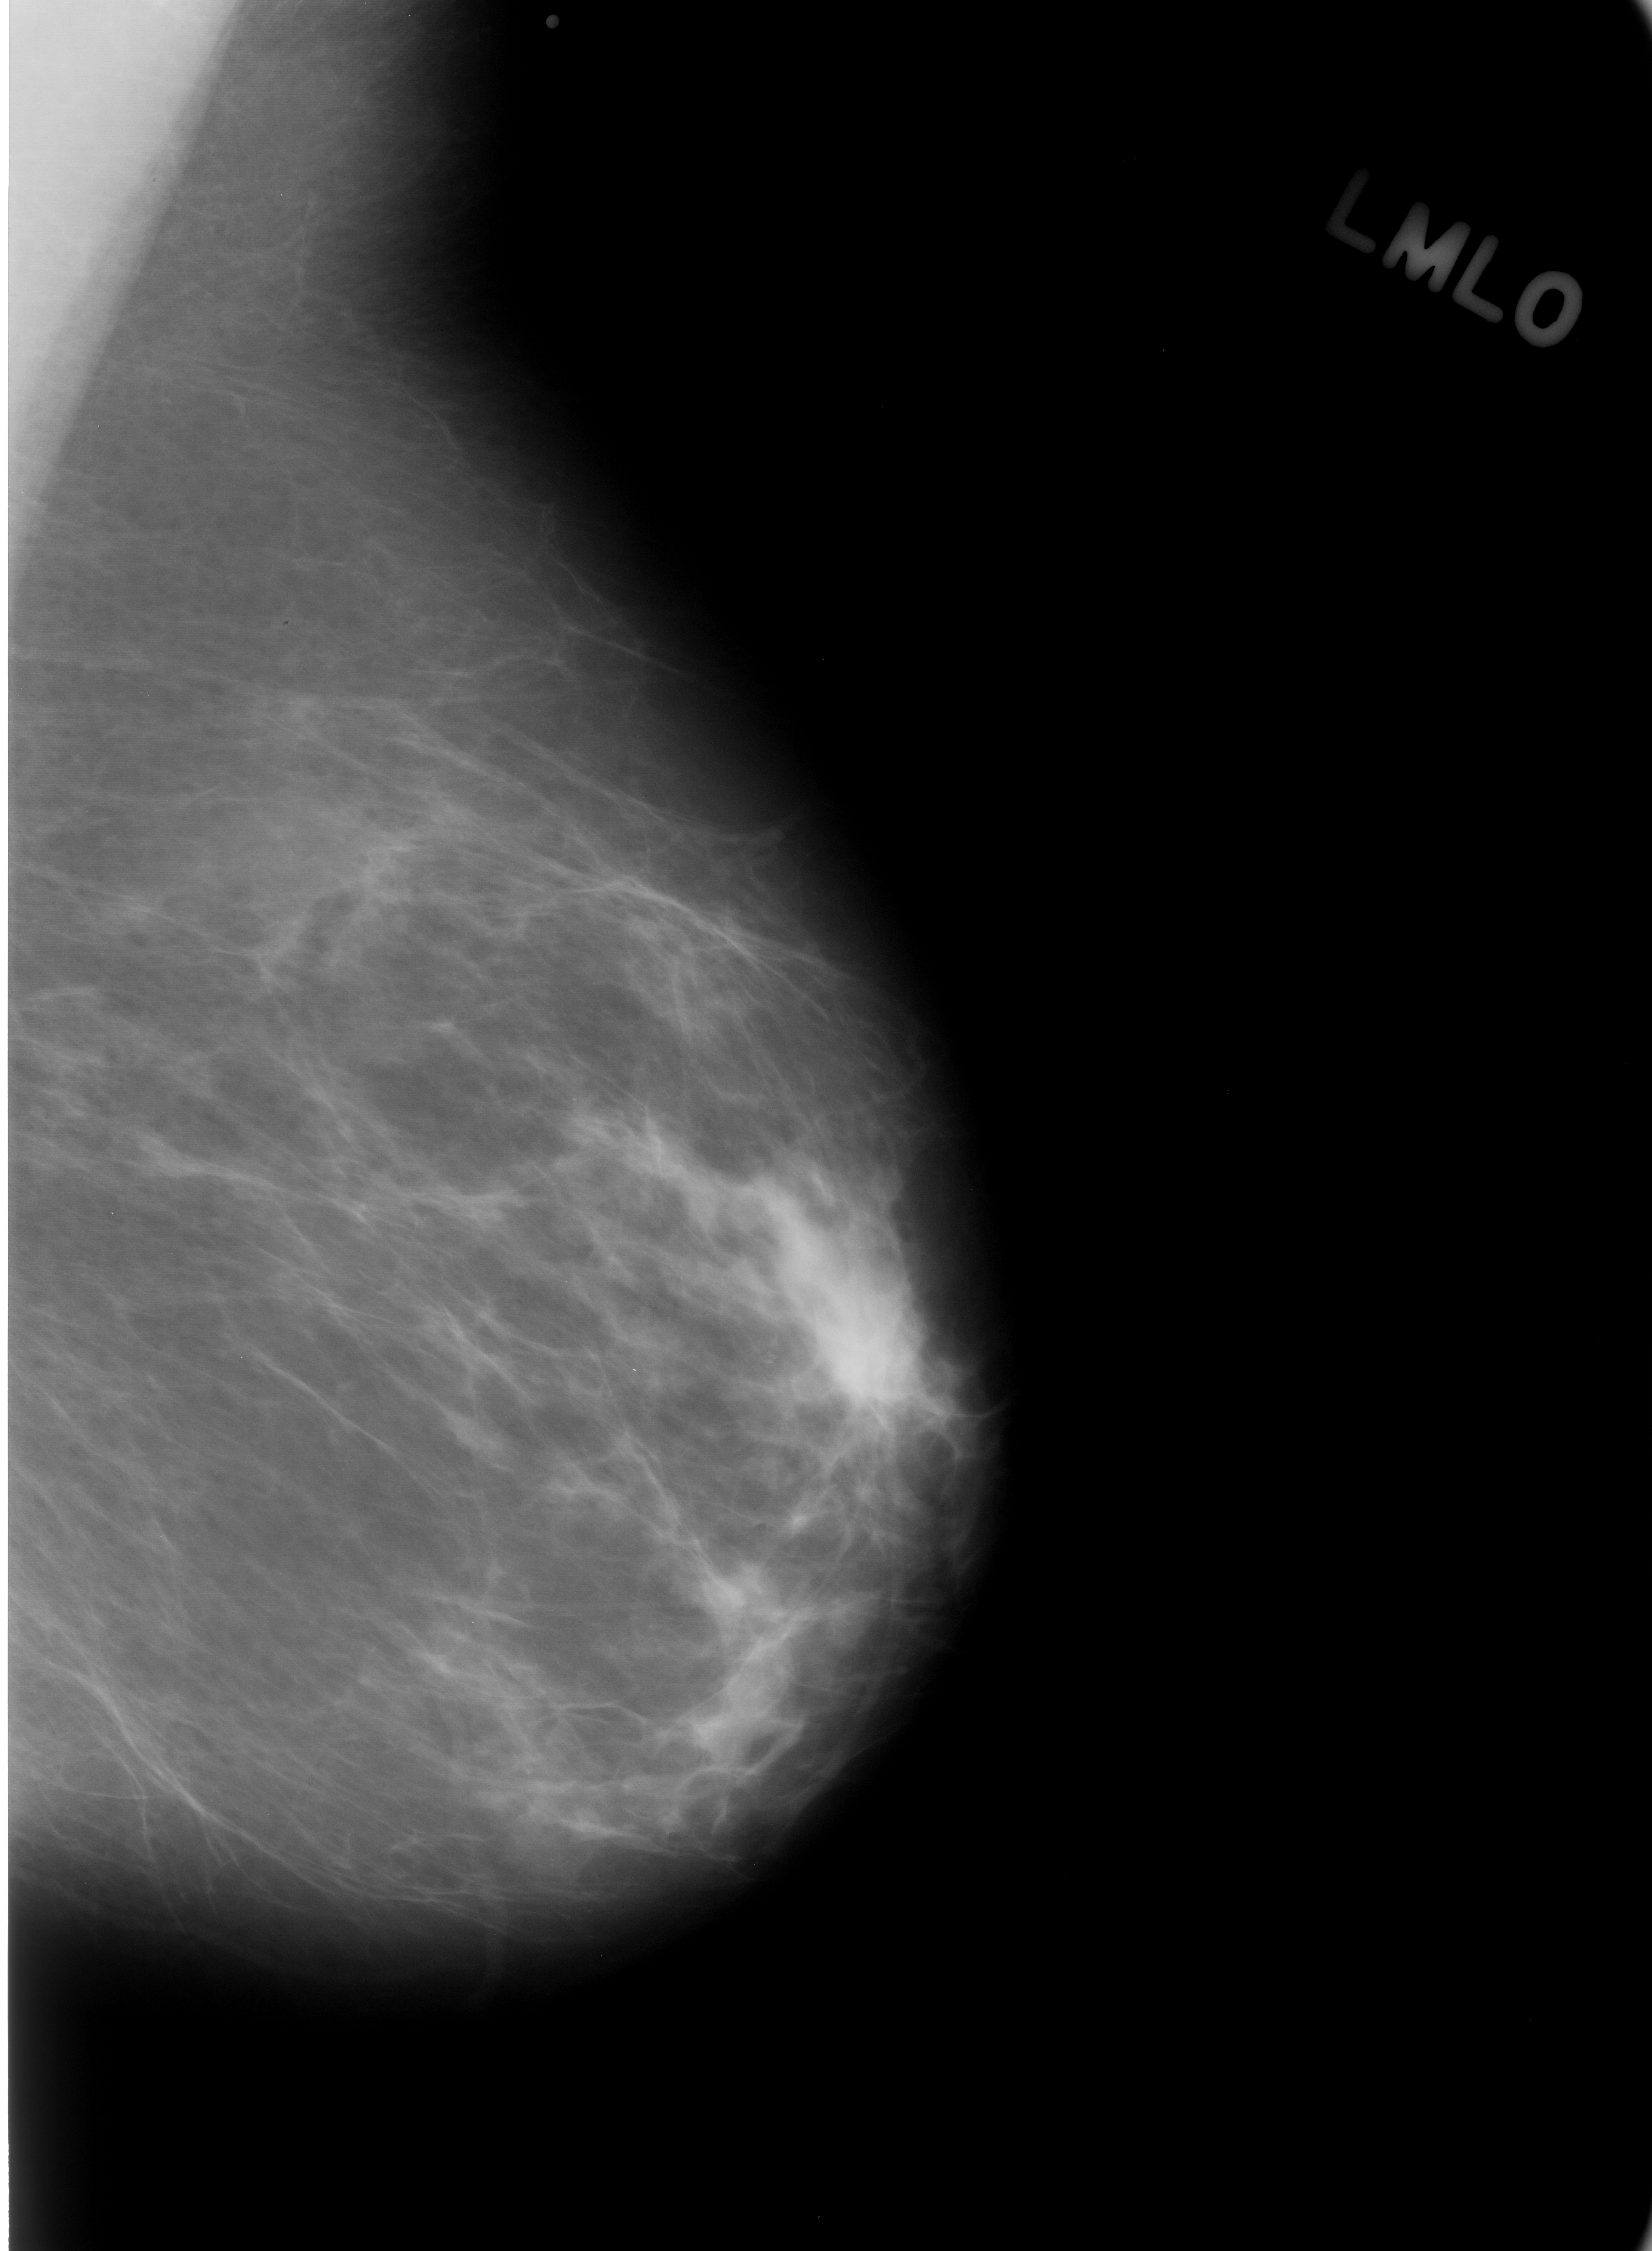
Scanned film-screen mammogram, left breast, mediolateral oblique (MLO) view, BI-RADS breast density category 2 (scale 1–4).
- Radiologist-marked abnormalities on this image: calcifications, morphology pleomorphic, distribution clustered; BI-RADS assessment category 4; pathology (as recorded): benign.